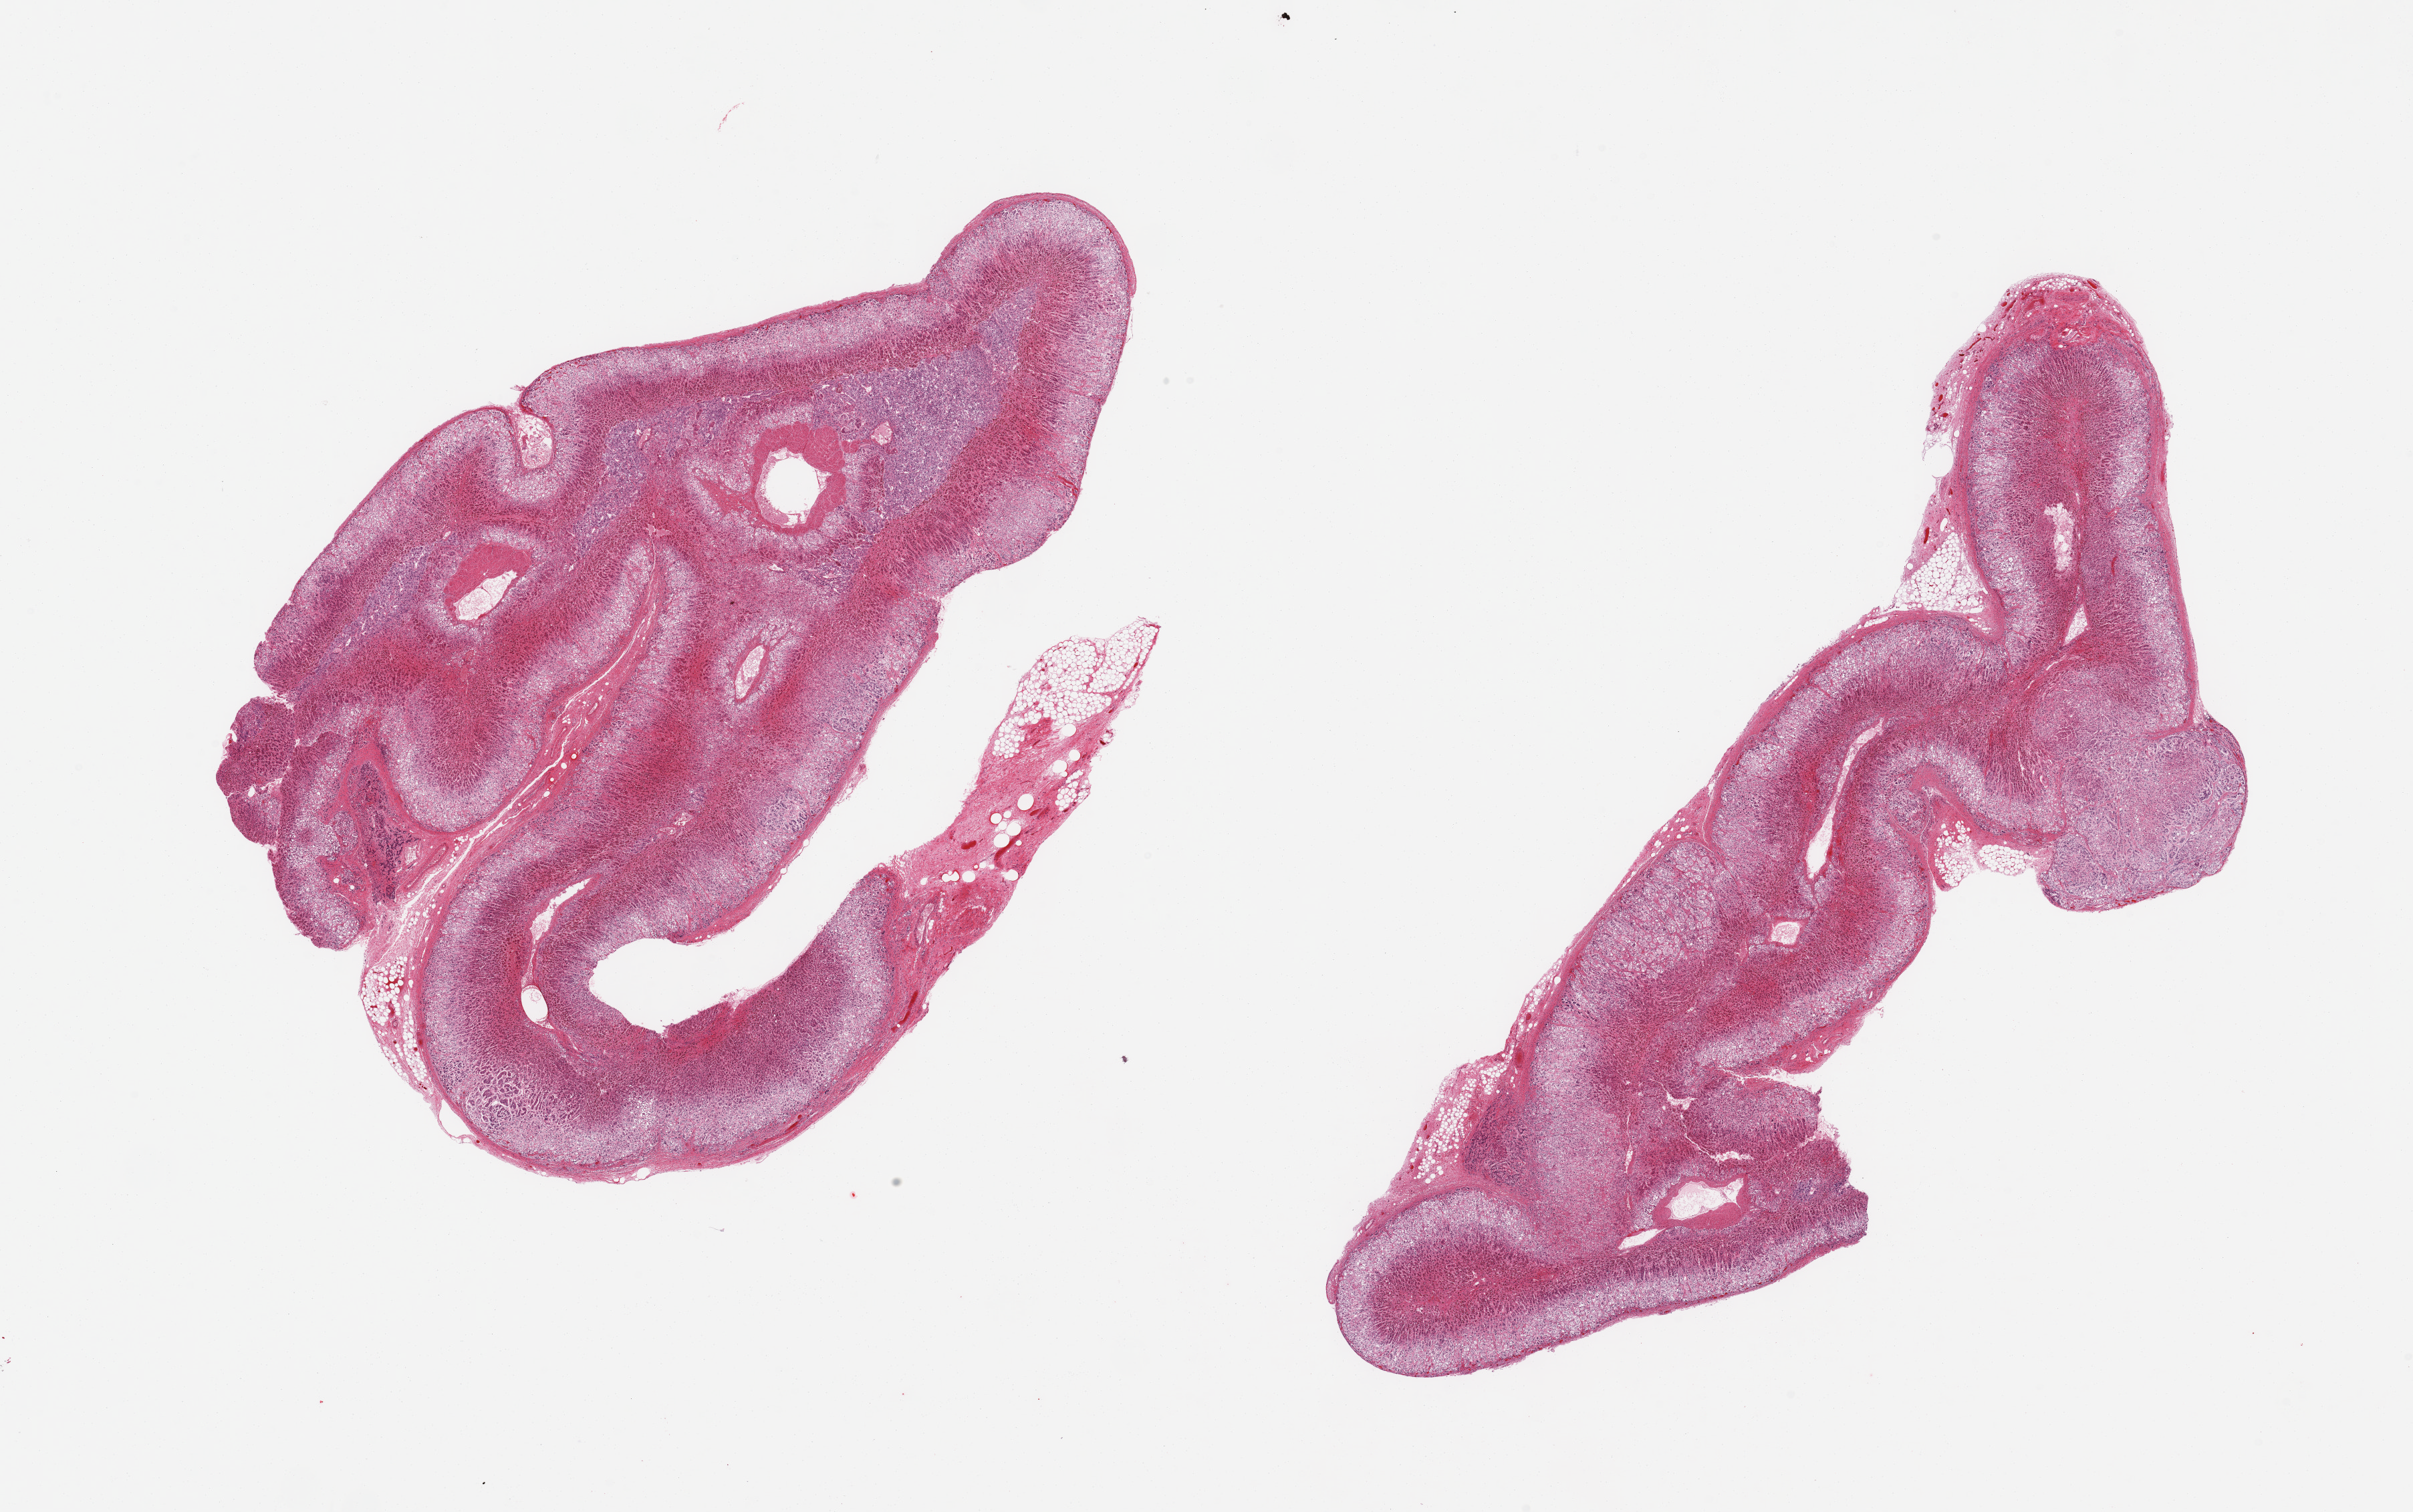
Whole-slide image, H&E stain, brightfield — a low-resolution overview of the entire scanned area, about 28.5 x 17.9 mm. PAXgene-fixed, paraffin-embedded tissue. Section of adrenal gland (target tissue). Donor tissue sample. Donor: male.
Pathologist's review note for this sample: 2 pieces; 10% external fat.